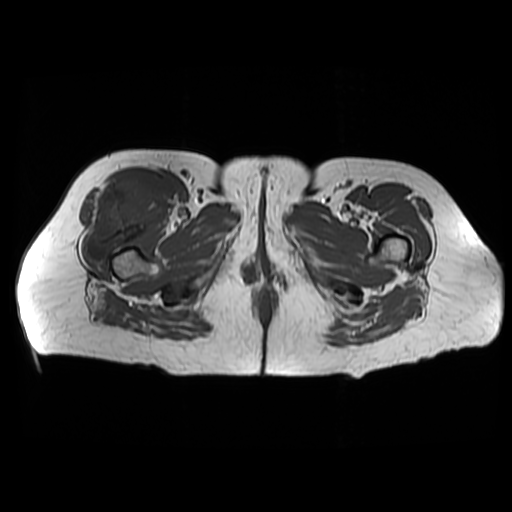
MRI of an extremity soft-tissue mass, one axial slice; position 37 of 48 along the scan axis; 6 mm slice thickness; 512 × 512 image matrix, field of view 440 × 440 mm. Female patient. Case-level facts recorded for this patient, not image findings: histological type: pleiomorphic undifferentiated sarcoma; grade: high; site of the primary tumour: right quadricep.
Structures marked on this image (outlined manually by an expert reader):
- gross tumour volume including surrounding oedema: bounding box [x1, y1, x2, y2] px = [81, 175, 168, 261]
- gross tumour volume (mass): [81, 175, 168, 261]